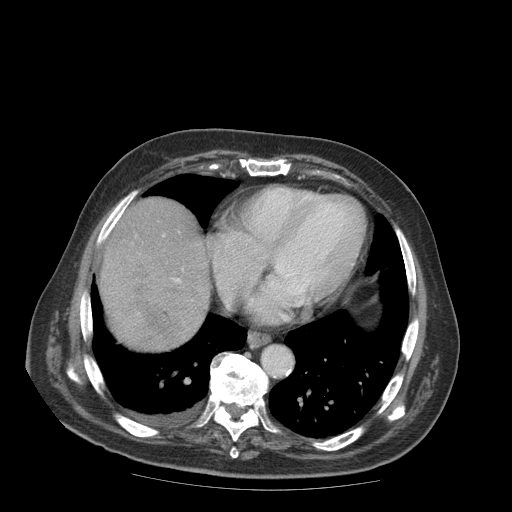
Contrast-enhanced abdominal CT (liver protocol), one axial slice. Position 85 of 99 along the scan axis. 140 kVp. Soft-tissue window (W 400 / L 40 HU). 512 × 512 image matrix. From the clinical record (not read from this slice): diagnosis: hepatocellular carcinoma (patient treated with transarterial chemoembolisation; whether this scan precedes or follows treatment is not stated here); TNM stage (as recorded): Stage-IIIB; Child-Pugh class: A; tumour nodularity: multinodular.
Annotated regions visible in this slice (semi-automatic segmentation, software-assisted and operator-edited):
- abdominal aorta: bounding box [x1, y1, x2, y2] px = [261, 345, 293, 376]
- liver parenchyma outside the tumour (the mass and vessels are separate outlines, so this box may not span the whole liver): [98, 198, 208, 317]
- mass: [99, 250, 207, 351]
- liver vessels: [163, 235, 181, 282]